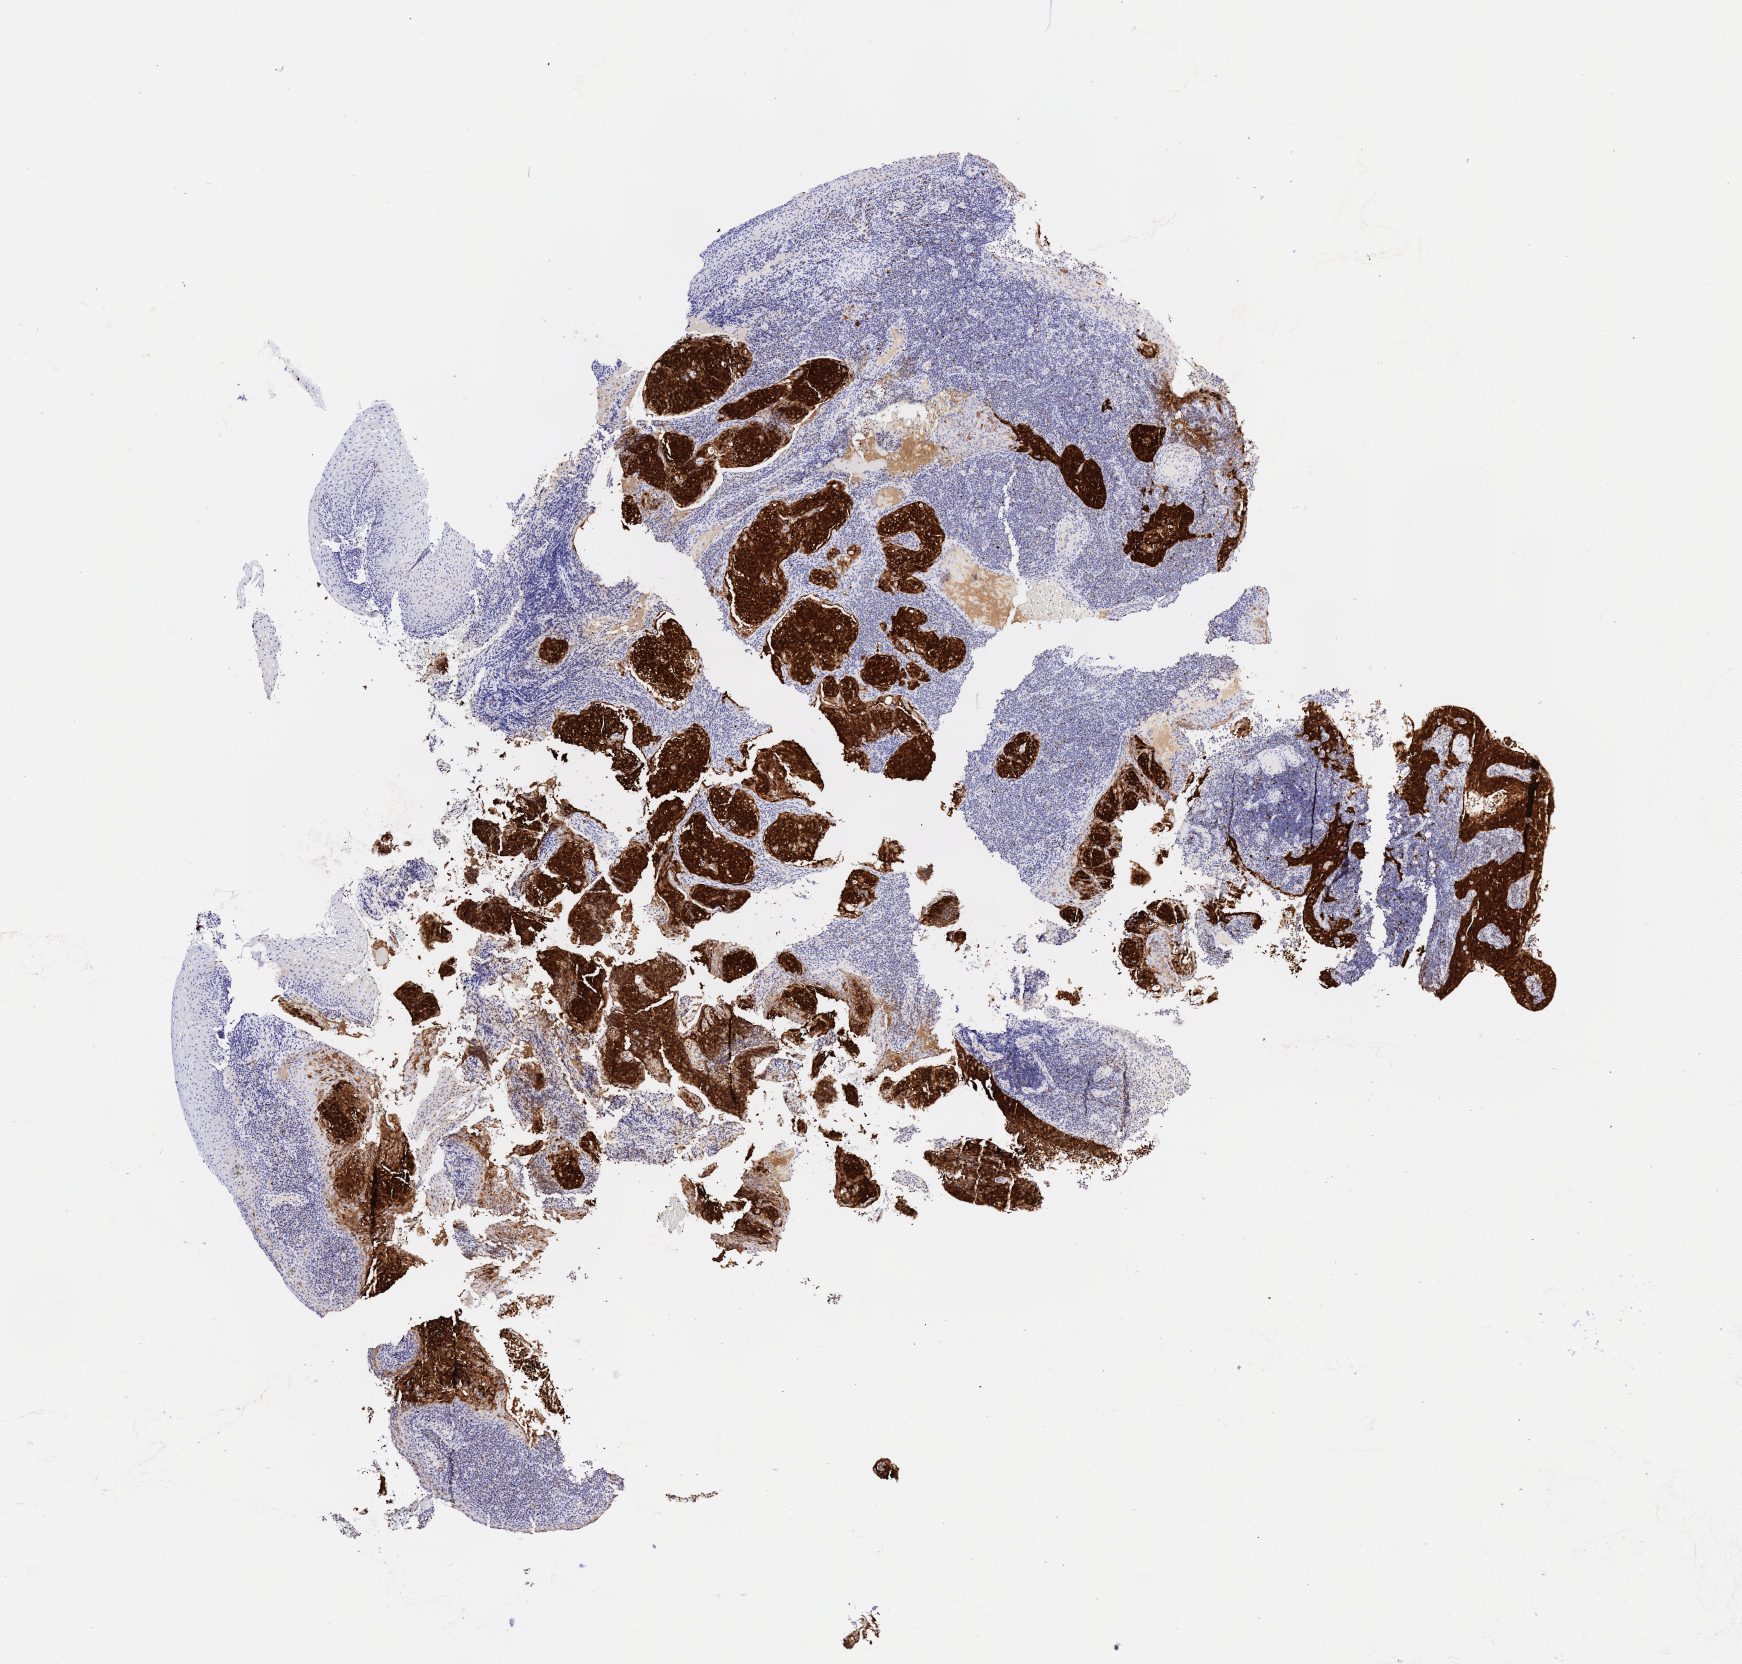
Immunohistochemistry (IHC) whole-slide image stained for p16 (p16INK4a), a low-resolution overview of the entire scanned area, about 7.0 x 6.7 mm. Specimen: tumor tissue. Anatomic site: cervix. Female patient, age 44 years.
Histologic diagnosis: Squamous cell carcinoma, large cell, nonkeratinizing, NOS.